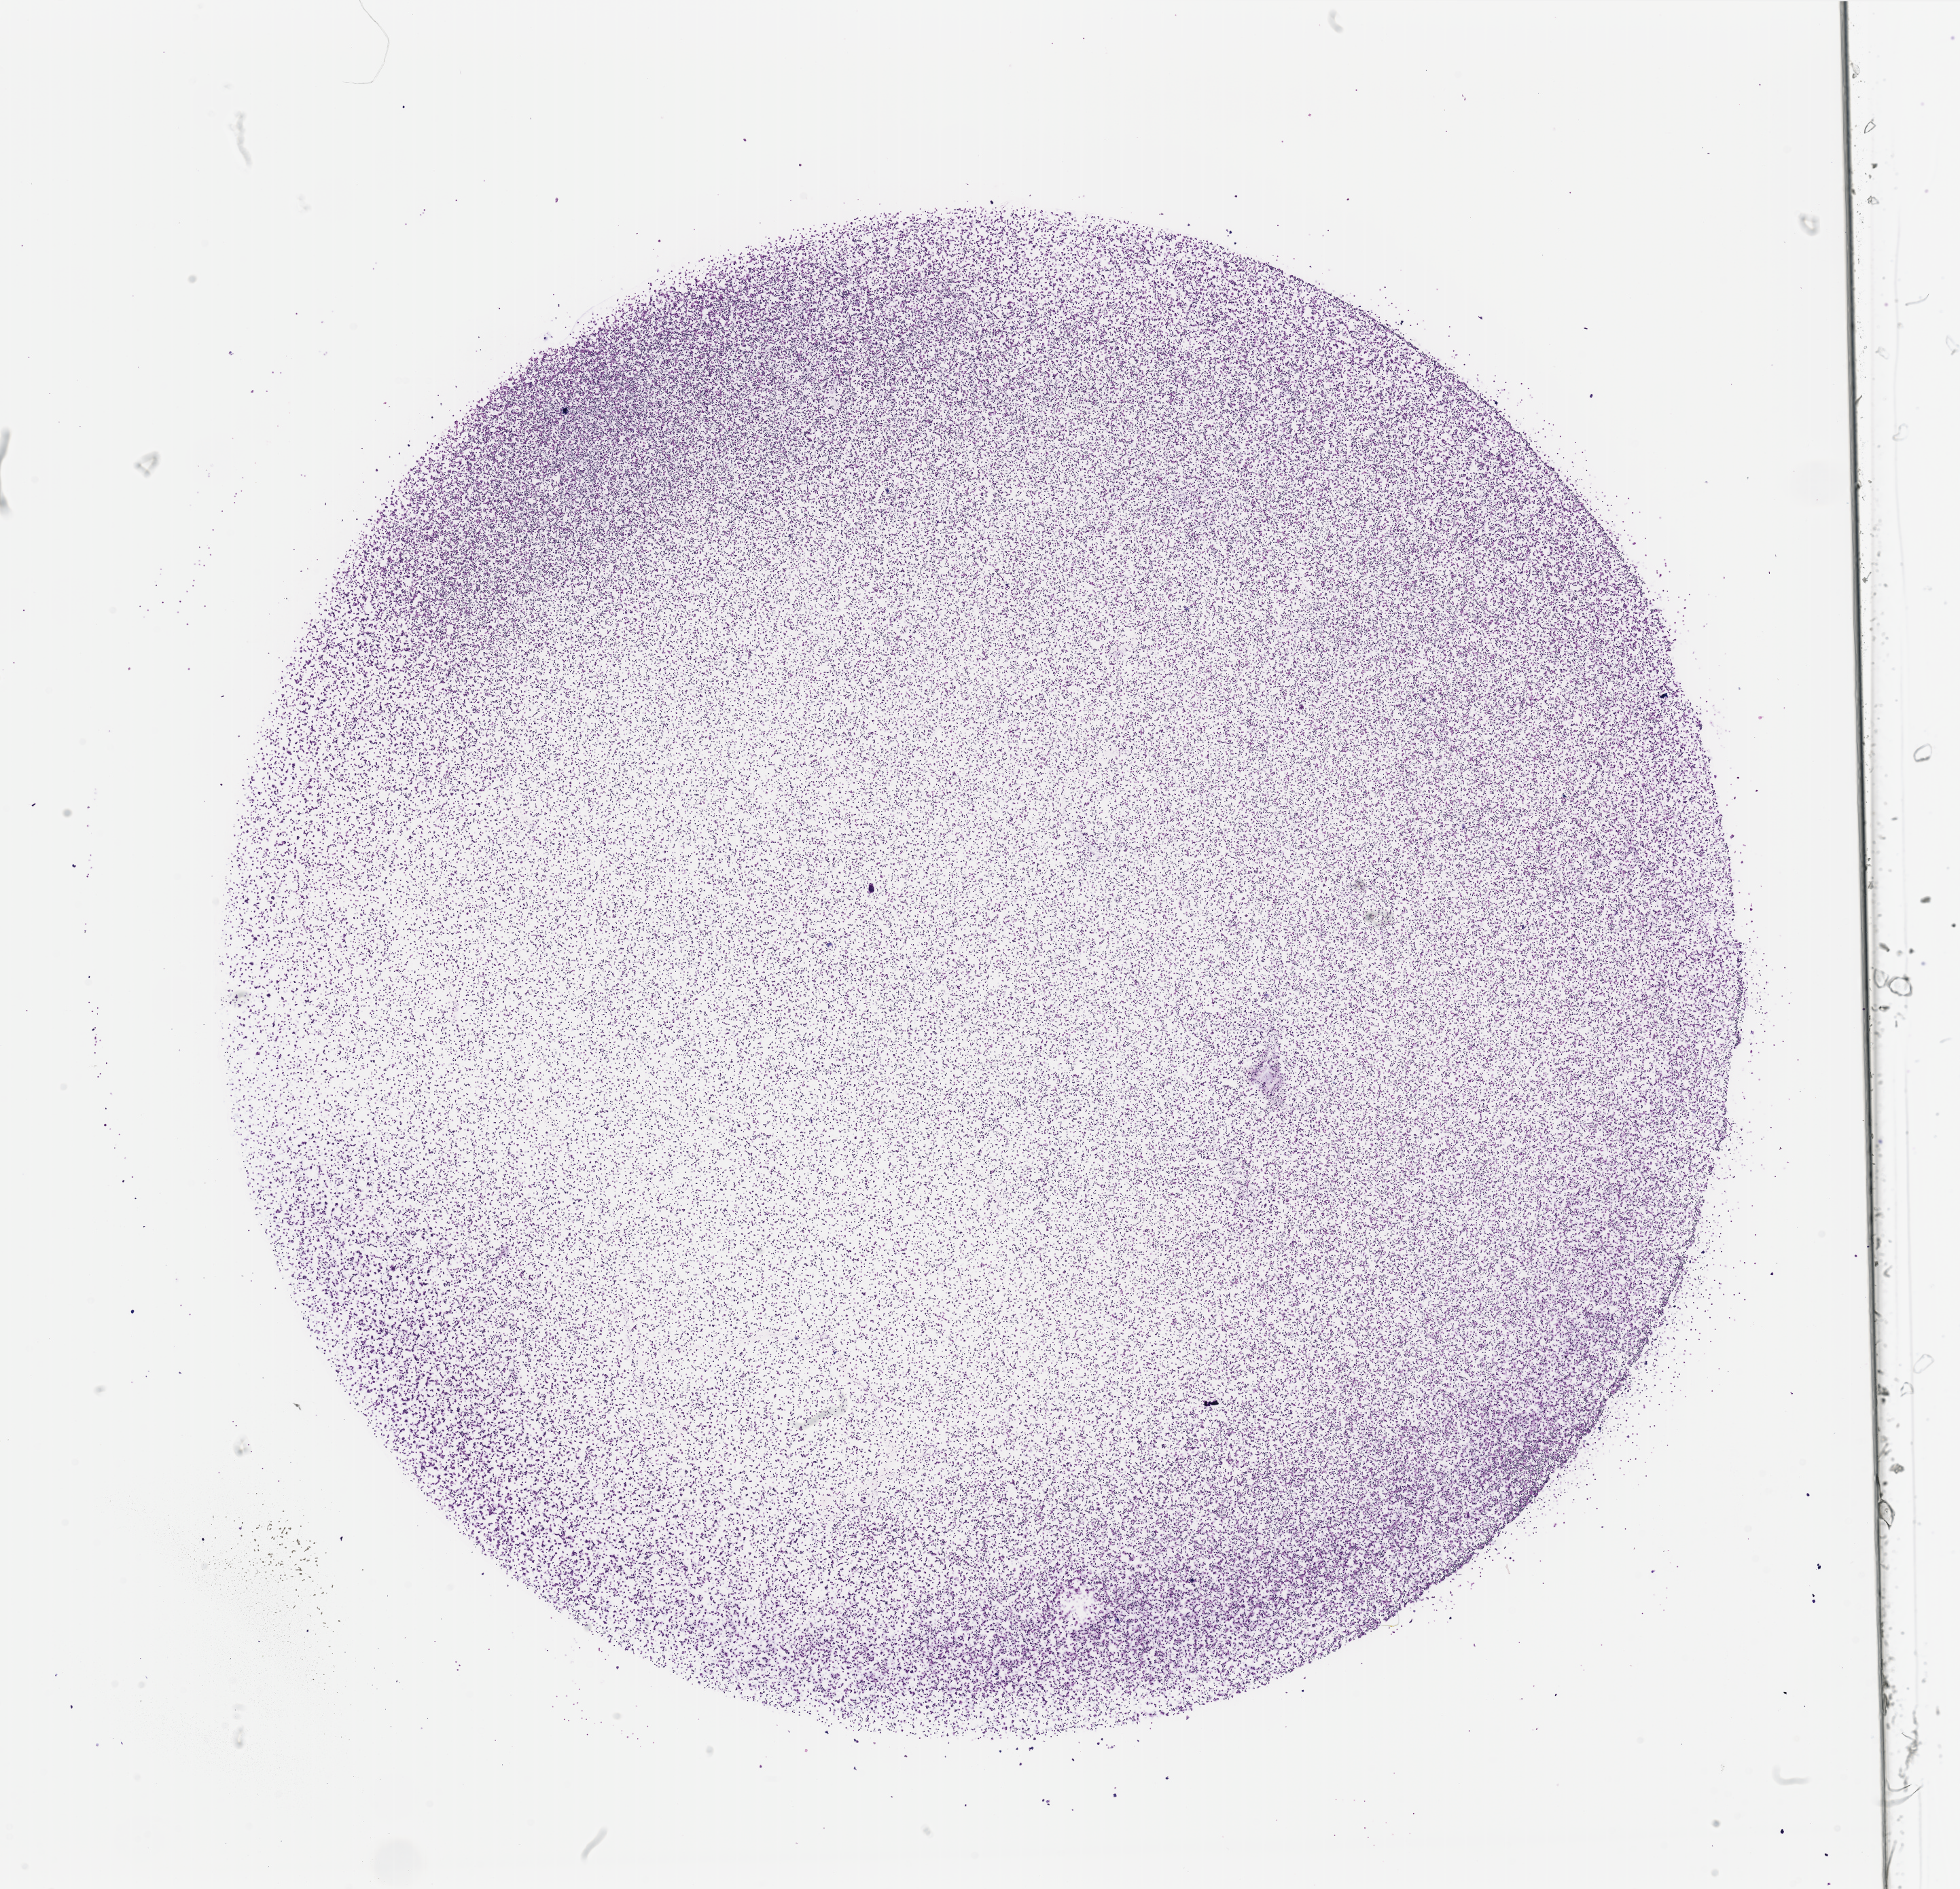
Whole-slide histology image, Hematoxylin and eosin (H&E) stained — shown as a low-resolution overview of the whole scanned area (about 22.8 x 22.0 mm); bone marrow (leukaemic) sample. Patient: male, age 53 years. Blasts: 90%.
* WHO classification: Acute Promyelocytic Leukemia with t(15;17)(q22;q12); PML-RARA
* diagnosis: Acute Myeloid Leukemia
* FAB classification: M3